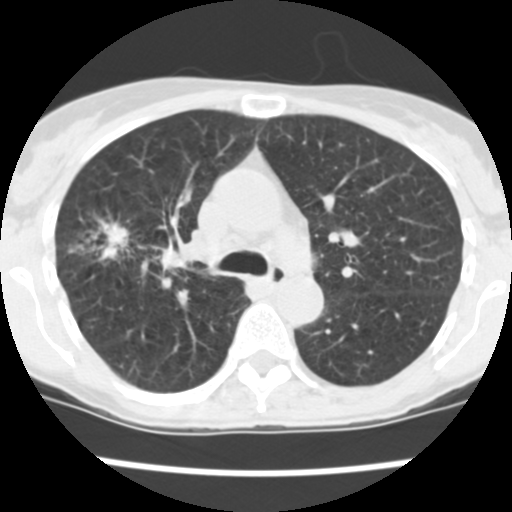
Low-dose screening chest CT, axial slice, first (baseline) screen, lung window (W 1500 / L -600 HU), slice 162 of 252 in the series, 512 × 512 image matrix, field of view 276 × 276 mm. Female, age 60 years at enrolment. Current smoker at enrolment.
- Lesion marked by an expert reader, bounding box [x1, y1, x2, y2] px = [82, 216, 189, 282].
- The screening reader recorded 3 non-calcified nodules or masses ≥4 mm on this exam (right upper lobe, right upper lobe, right lower lobe); which of them this box marks is not recorded.
- Lung cancer was diagnosed 19 days after this screen: non-small cell carcinoma, right upper lobe, stage IV (AJCC 6th edition), 26 mm at pathology.